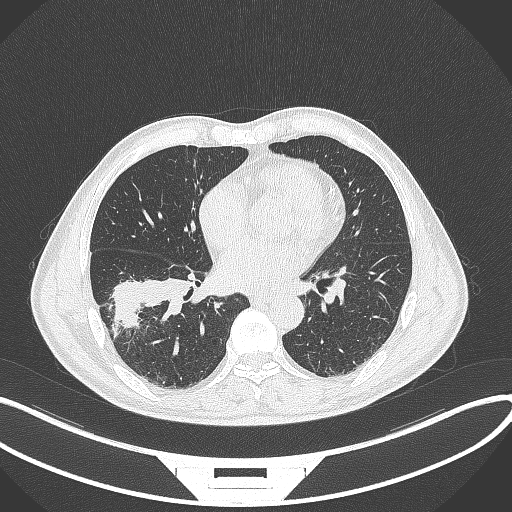
Chest CT, one axial slice. Slice 159 of 364 in the series (ordered by position). 120 kVp. Lung window (W 1500 / L -600 HU). 512 × 512 image matrix, field of view 400 × 400 mm. Patient: male, 58 years. From the clinical record (not read from this slice): clinical TNM (as recorded): T3 N0 M0; histopathological grade: G2.
Annotated regions visible in this slice (bounding box drawn by a radiologist):
- lung tumour (recorded histology: squamous cell carcinoma): box from (x=110, y=275) to (x=192, y=328) px